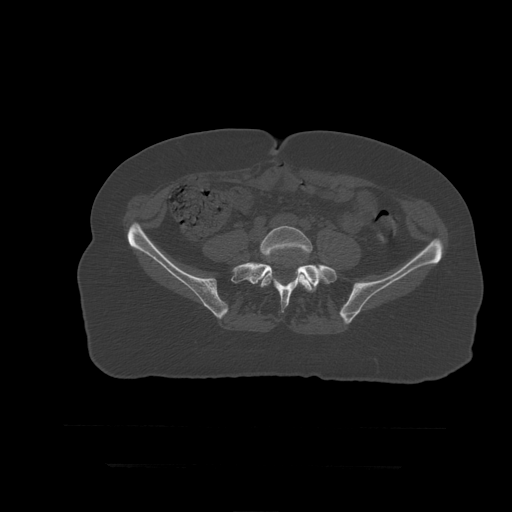
CT including the spine, one axial slice; slice 62 of 399 in the series (ordered by position); reconstruction kernel STANDARD; bone window (W 1800 / L 400 HU); 512 × 512 image matrix, field of view 450 × 450 mm. Patient age 41 years. Case-level facts recorded for this patient, not image findings: primary cancer: breast.
Annotated regions visible in this slice (semi-automatic segmentation, software-assisted and operator-edited):
- L5 vertebra: bounding box (x1, y1, x2, y2) in pixels: (260, 226, 316, 293)